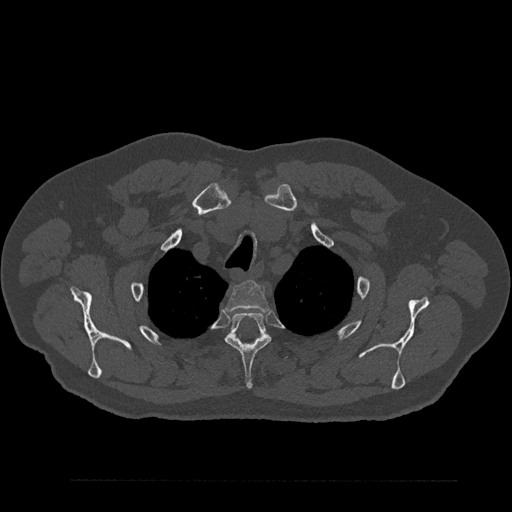
CT including the spine, one axial slice; slice 686 of 797 in the series (ordered by position); bone window (W 1800 / L 400 HU); 0.5 mm slice thickness; 512 × 512 image matrix, field of view 430 × 430 mm. Male patient, age 61 years. Case-level facts recorded for this patient, not image findings: primary cancer: prostate.
Outlined on this slice (semi-automatically segmented with operator editing):
- T2 vertebra: bounding box (x1, y1, x2, y2) in pixels: (226, 280, 269, 312)
- T3 vertebra: (225, 312, 272, 389)
- T4 vertebra: (234, 336, 288, 361)